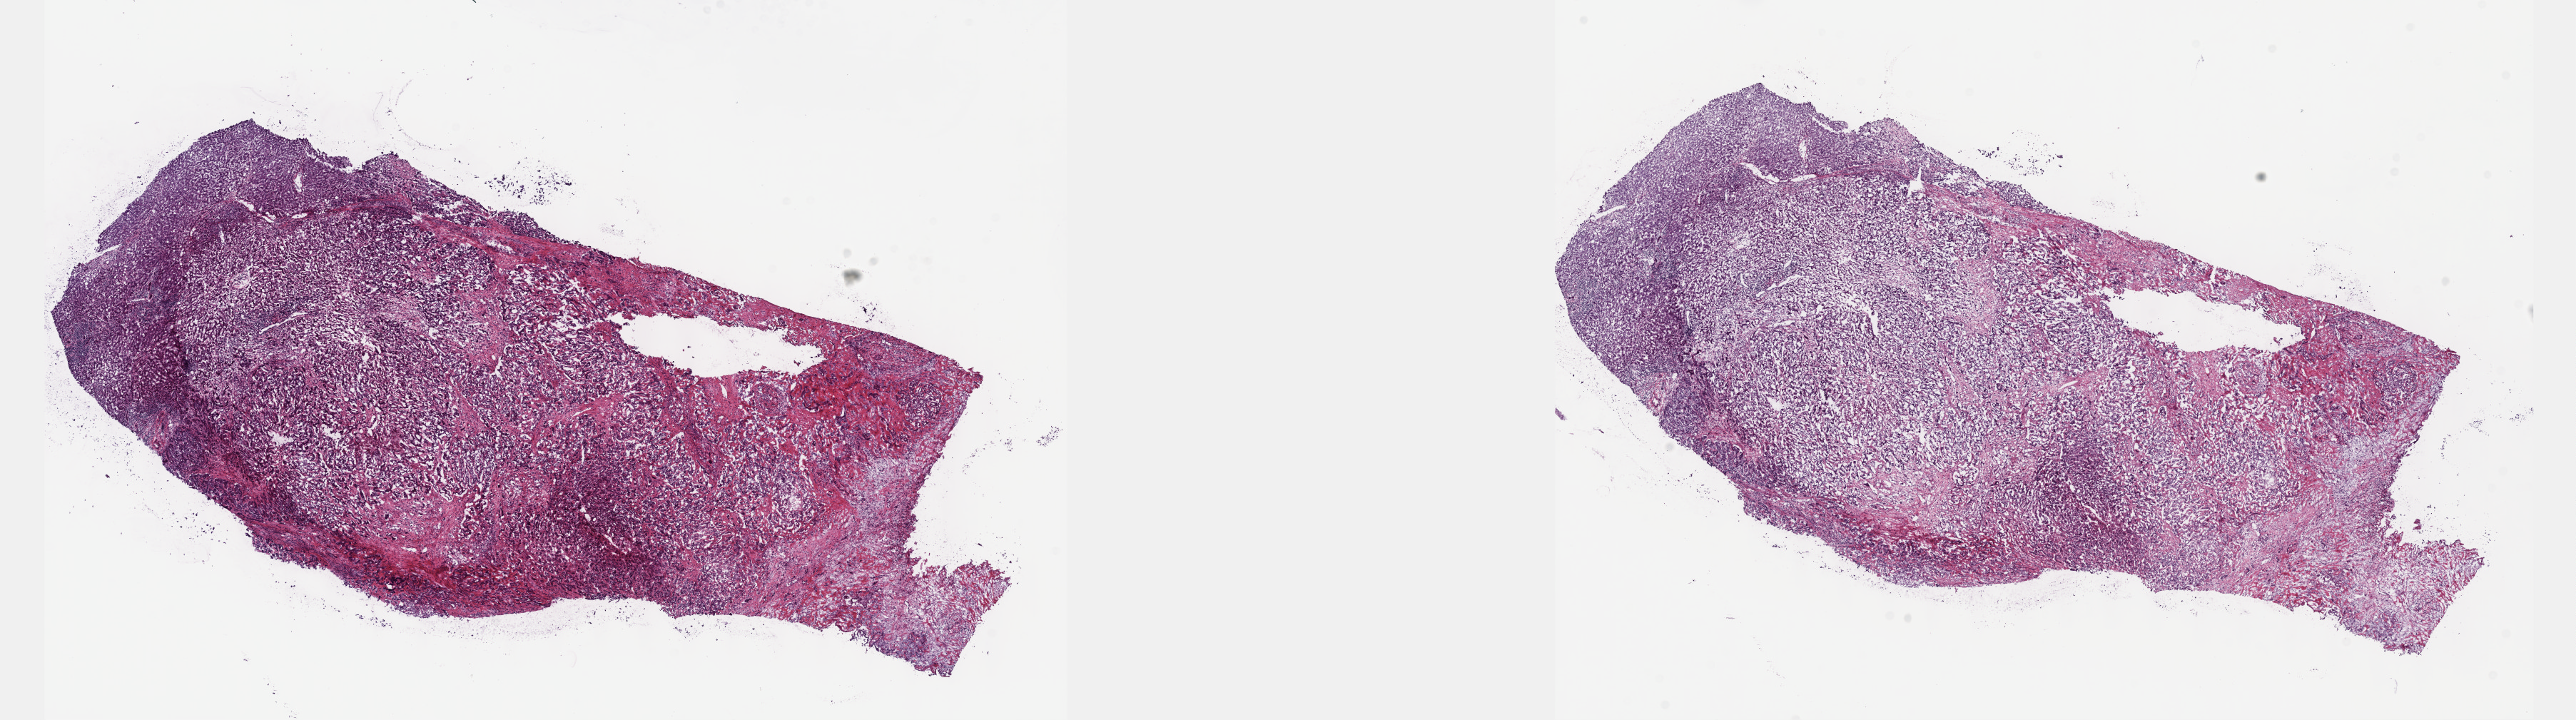
Digitized H&E tissue section (whole slide), a low-resolution overview of the entire scanned area, about 29.2 x 8.2 mm (slide scanned at 40x). Pathologist review of this section (percent, as recorded): tumour cells 70%, tumour nuclei 70%, normal cells 0%, stromal cells 28%, necrosis 2%. Infiltration values recorded for this section: lymphocyte infiltration 5%, monocyte infiltration 2%, neutrophil infiltration 4%.
Specimen: frozen section from the top of the tissue portion; sample: primary tumour, bile duct.